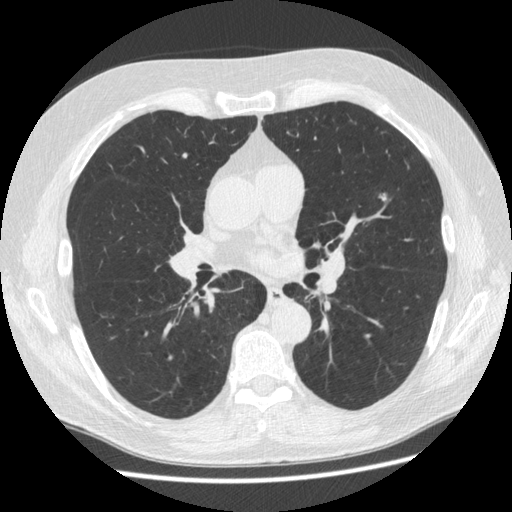
Low-dose screening chest CT, one axial slice; position 299 of 545 along the scan axis; reconstruction kernel STANDARD; lung window (W 1500 / L -600 HU); 1.25 mm slice thickness; 512 × 512 image matrix, field of view 360 × 360 mm.
Outlined on this slice (outlined manually by an expert reader):
- lesion 1 (nodule, upper lobe of left lung): box from (x=381, y=194) to (x=386, y=201) px